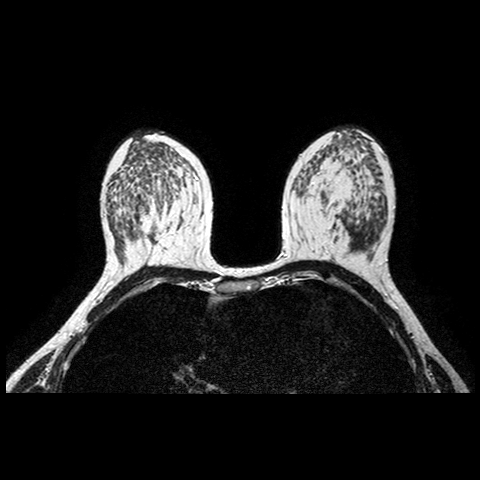
Breast MRI examination; 2 images, each one mid-volume slice chosen by position.
Image 1: fluid-sensitive (T2/STIR) axial slice, slice 43 of 84, 2 mm slice thickness.
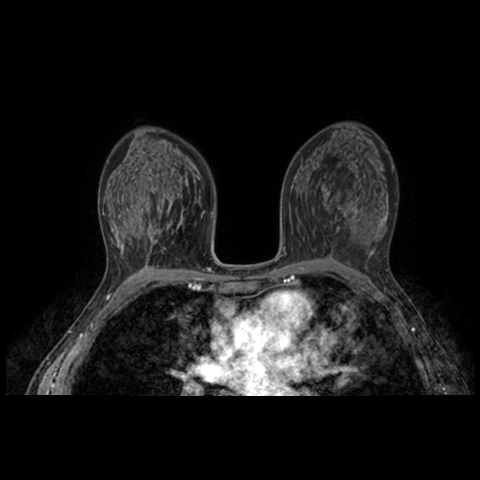
Image 2: post-contrast dynamic axial slice, slice 43 of 84, dynamic phase 6 of 10, 4 mm slice thickness.
Pathology recorded for this patient (not read from these images): pathology diagnosis: benign fibrocyst (left breast).